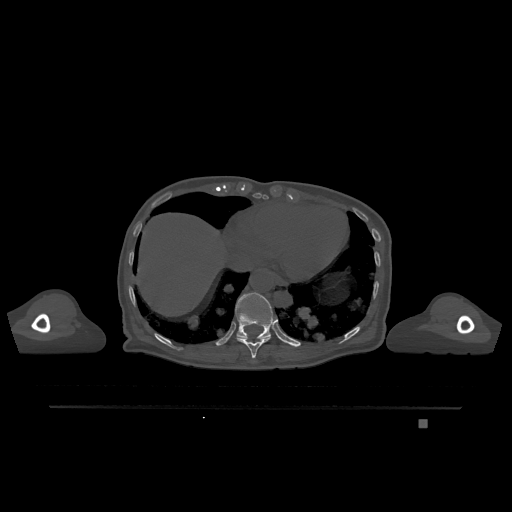
CT including the spine, one axial slice; slice 617 of 1317 in the series (ordered by position); bone window (W 1800 / L 400 HU); 0.5 mm slice thickness; 512 × 512 image matrix, field of view 500 × 500 mm. Patient: female, 74 years. Case-level facts recorded for this patient, not image findings: primary cancer: lung; vertebrae with lytic lesions (as recorded): T1, T4, T5, T6, L4, L5.
Structures marked on this image (semi-automatically segmented with operator editing):
- T10 vertebra: box from (x=236, y=337) to (x=271, y=359) px
- T11 vertebra: (x=235, y=292)–(x=276, y=339)